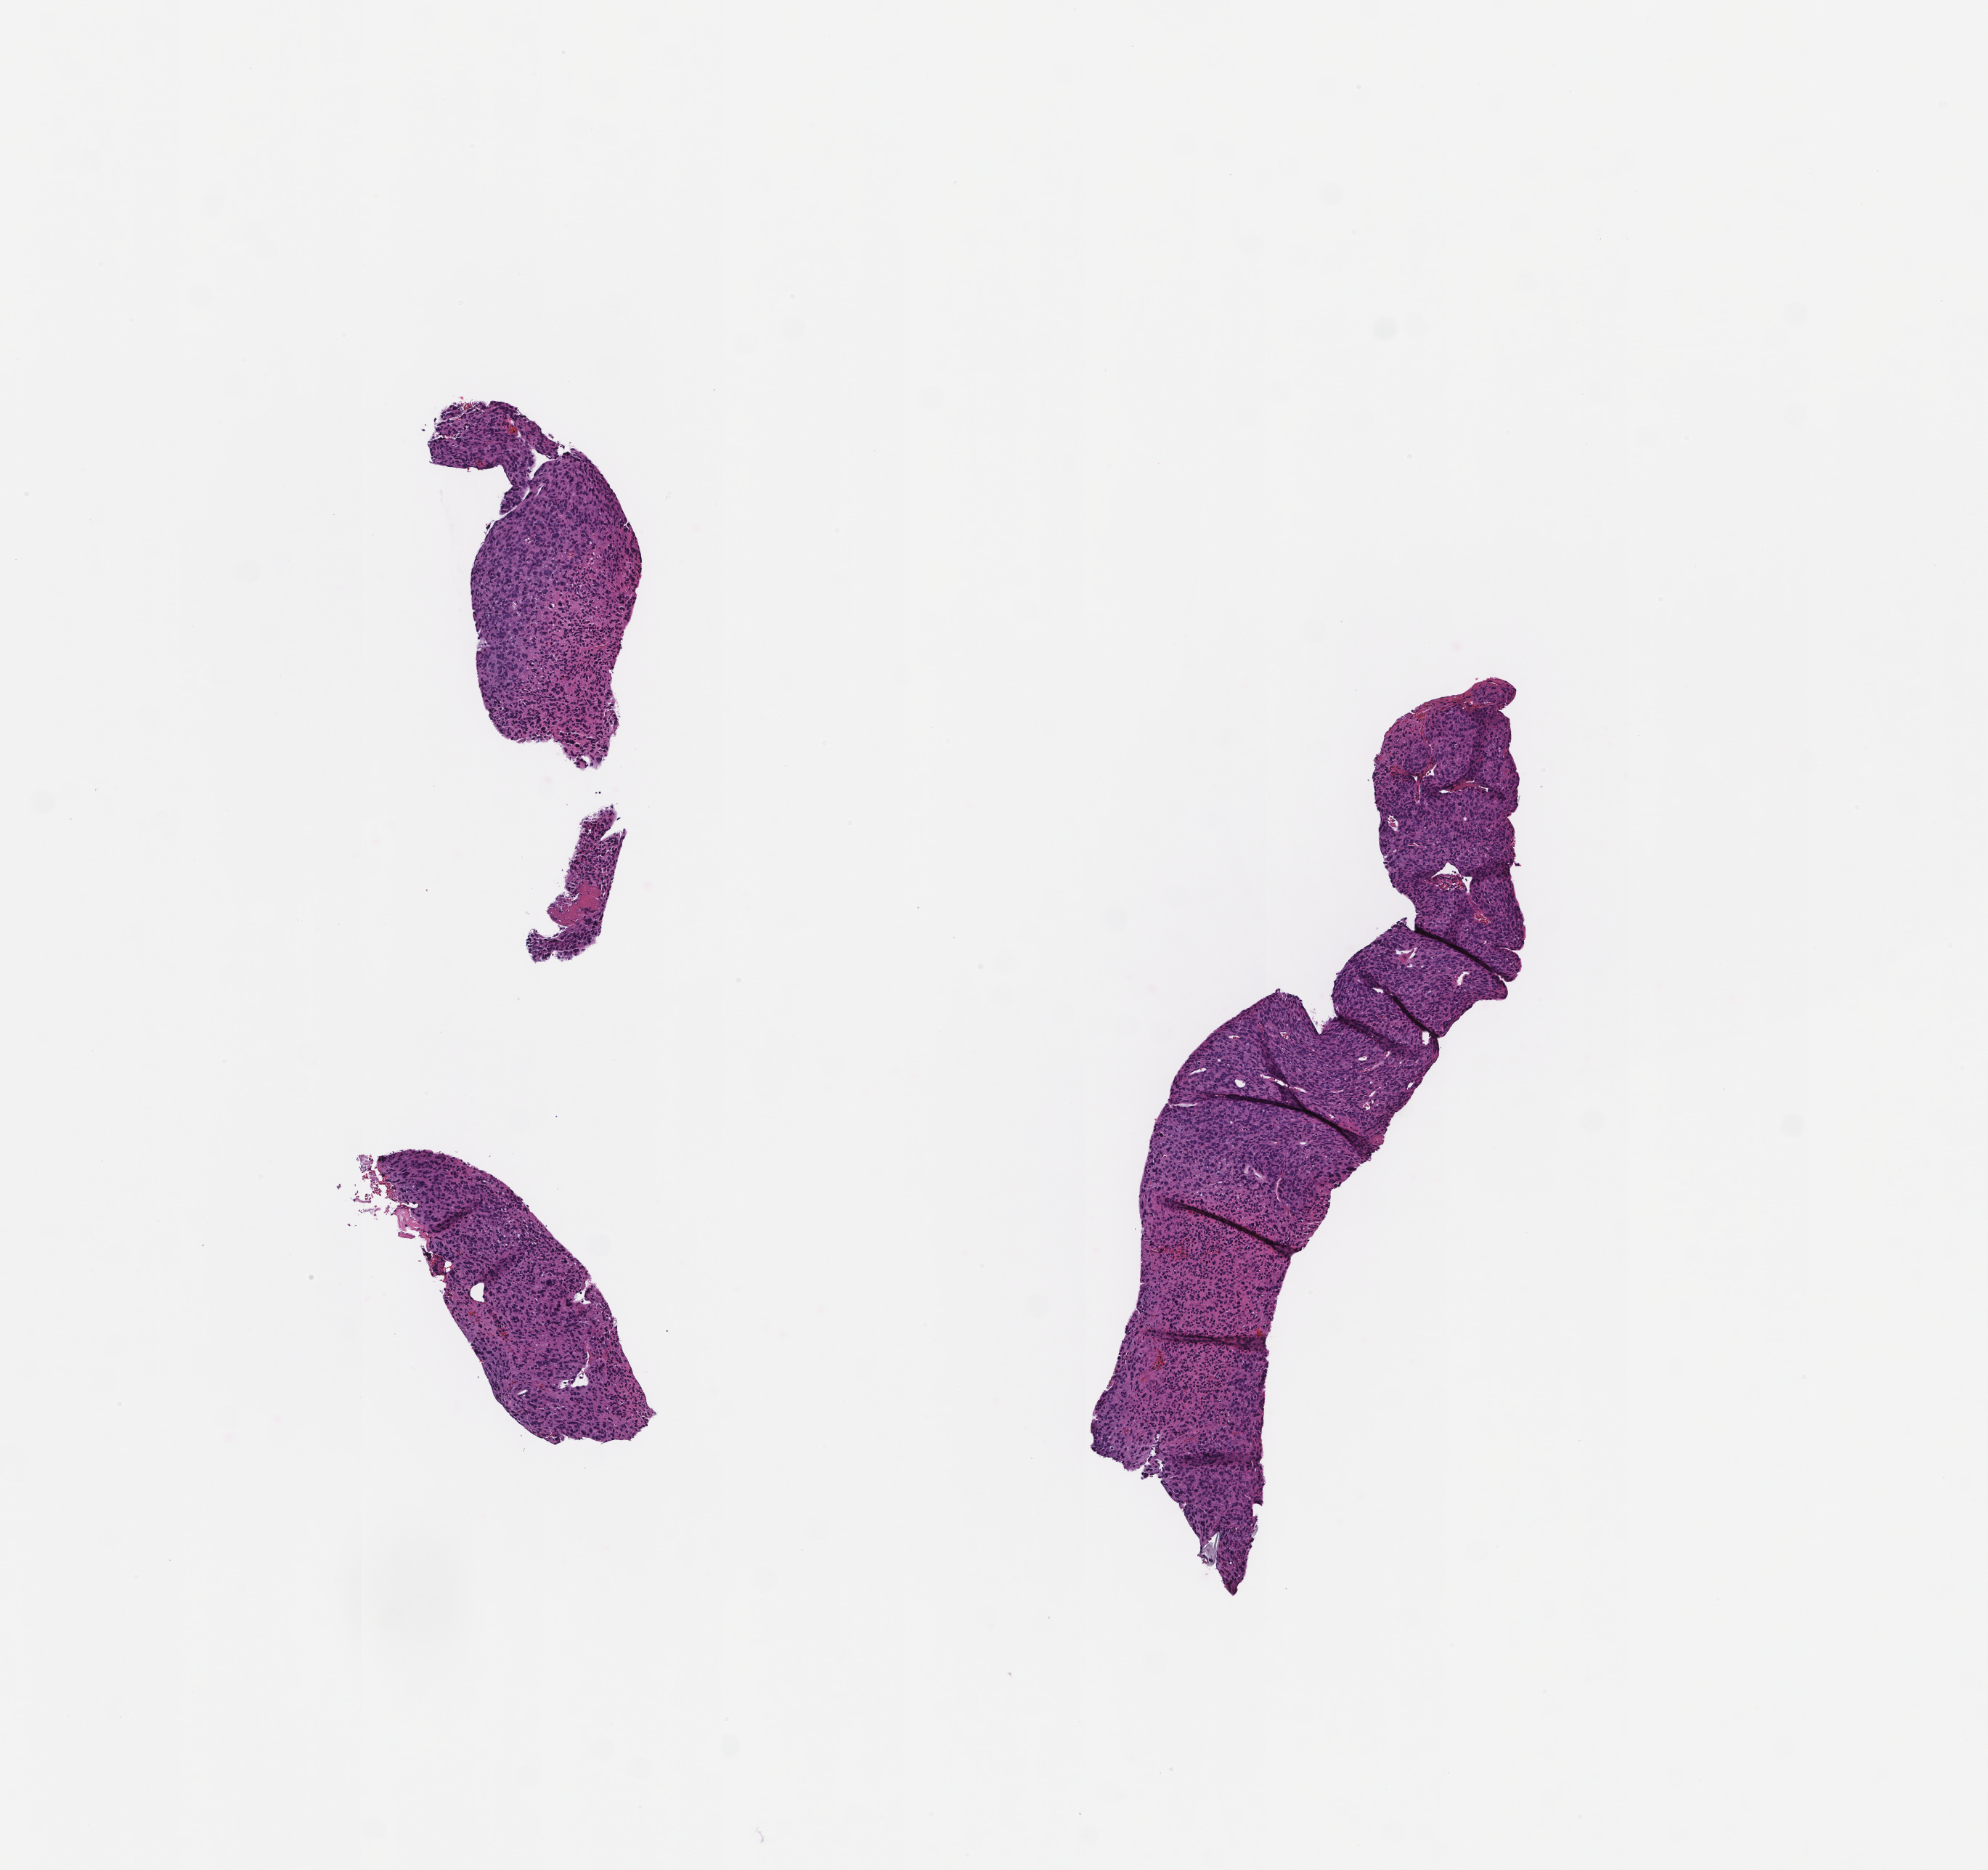
Digitized haematoxylin and eosin-stained section, a low-resolution overview of the entire scanned area, about 5.5 x 5.2 mm; formalin-fixed, paraffin-embedded (FFPE) tissue. Patient sex: female.
This section: metastasis (sampled organ not recorded). Primary diagnosis of the patient: Invasive Breast Carcinoma.